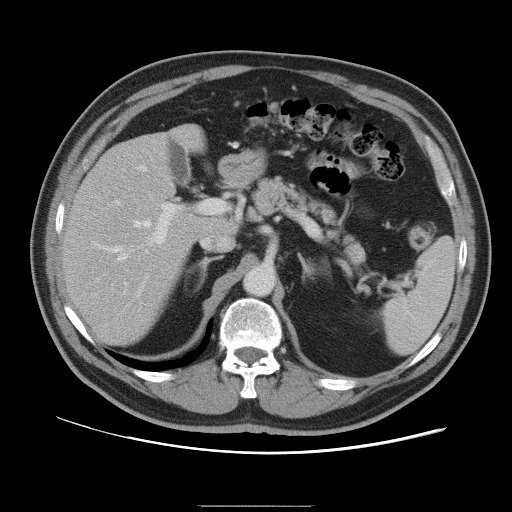
Contrast-enhanced abdominal CT, one axial slice. Position 60 of 105 along the scan axis. 120 kVp. Intravenous contrast given. Soft-tissue window (W 400 / L 40 HU). 512 × 512 image matrix, field of view 399 × 399 mm. Male patient, age 64 years. From the clinical record (not read from this slice): diagnosis: colorectal cancer liver metastases, imaged before liver resection; multiple liver metastases: yes; largest metastasis: 3 cm.
Structures marked on this image (outlined manually by an expert reader):
- hepatic veins: box from (x=113, y=166) to (x=151, y=285) px
- liver: (x=64, y=127)–(x=232, y=345)
- planned liver remnant (the part of the liver to remain after resection): (x=64, y=135)–(x=233, y=344)
- portal vein (with intrahepatic branches): (x=115, y=200)–(x=181, y=318)